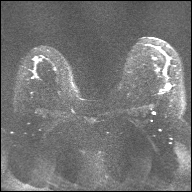
Breast MRI, one axial slice. Position 21 of 32 along the scan axis. Diffusion-weighted series; image 2 of 4 stored at this slice position (different b-values; order by instance number). 1.5 T. 192 × 192 image matrix, field of view 360 × 360 mm. Female patient.
Outlined on this slice (manually delineated by an expert):
- tumour on diffusion-weighted imaging: box from (x=167, y=85) to (x=169, y=89) px